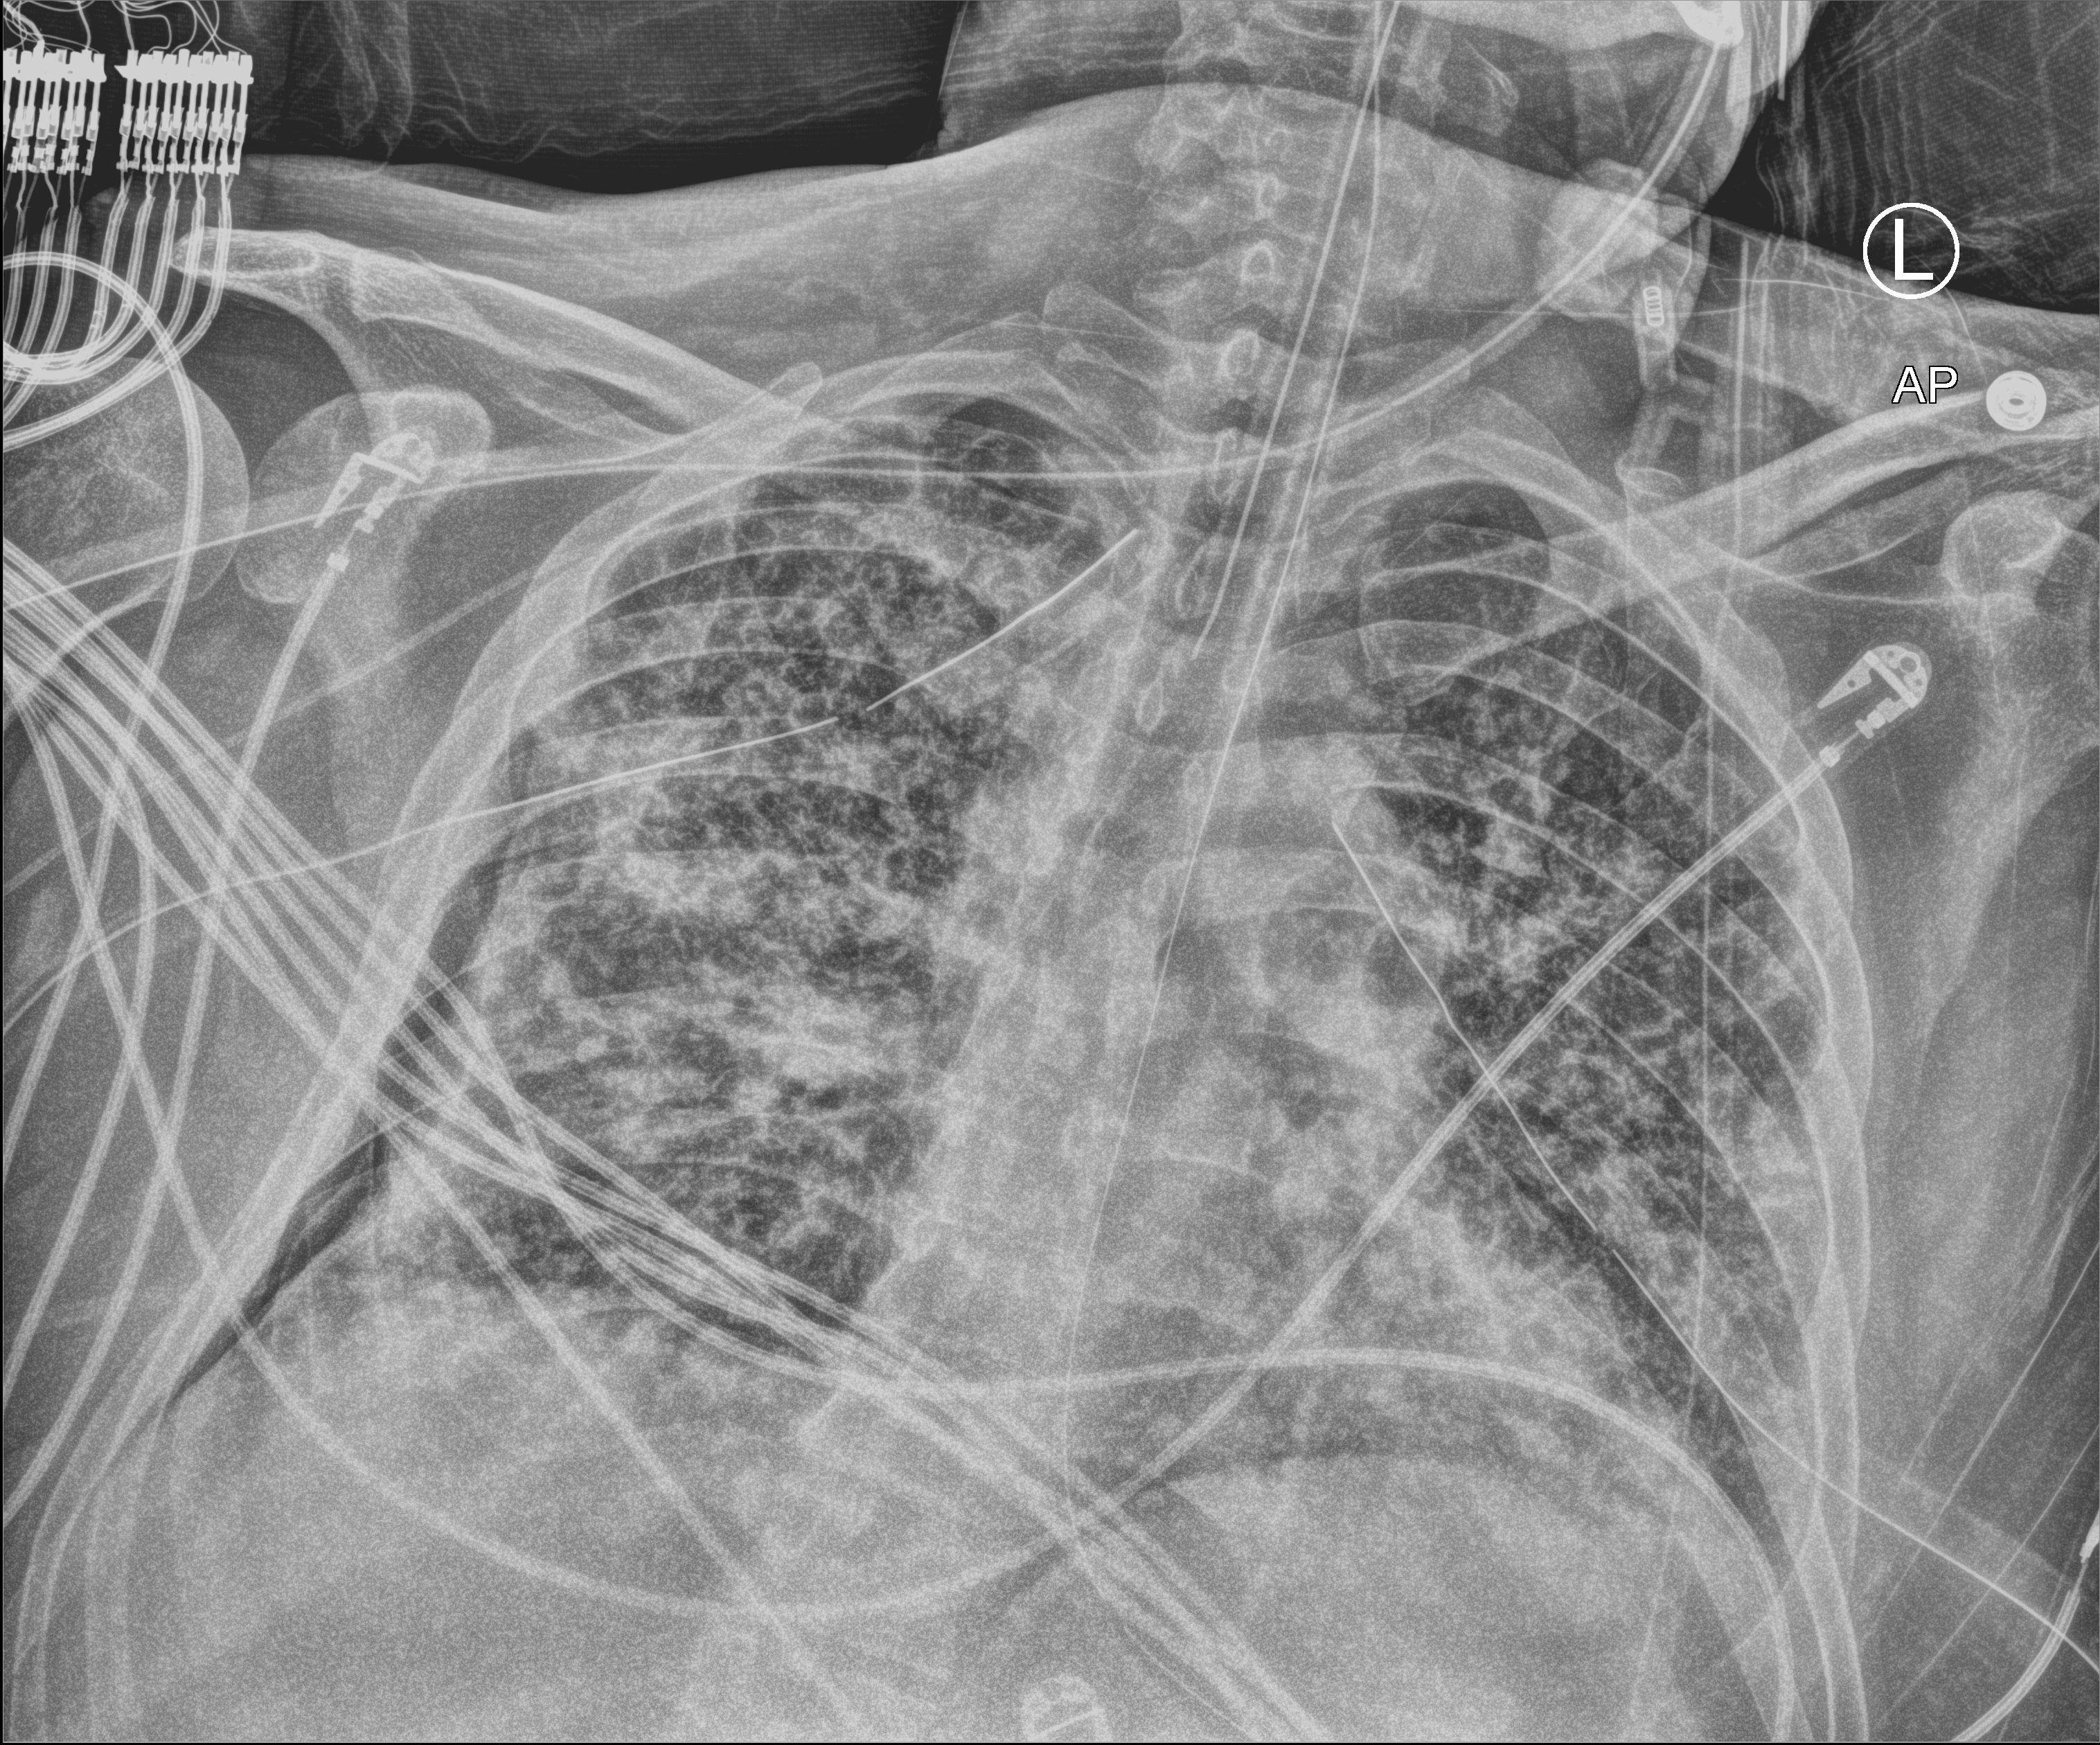
Bedside chest radiograph (computed radiography); anteroposterior (AP) projection. Male patient hospitalised with COVID-19, age 18–59 years.
Hospital-stay facts (about this admission, not read from this image; timing relative to this image not recorded):
- admitted to intensive care during this hospital stay: yes